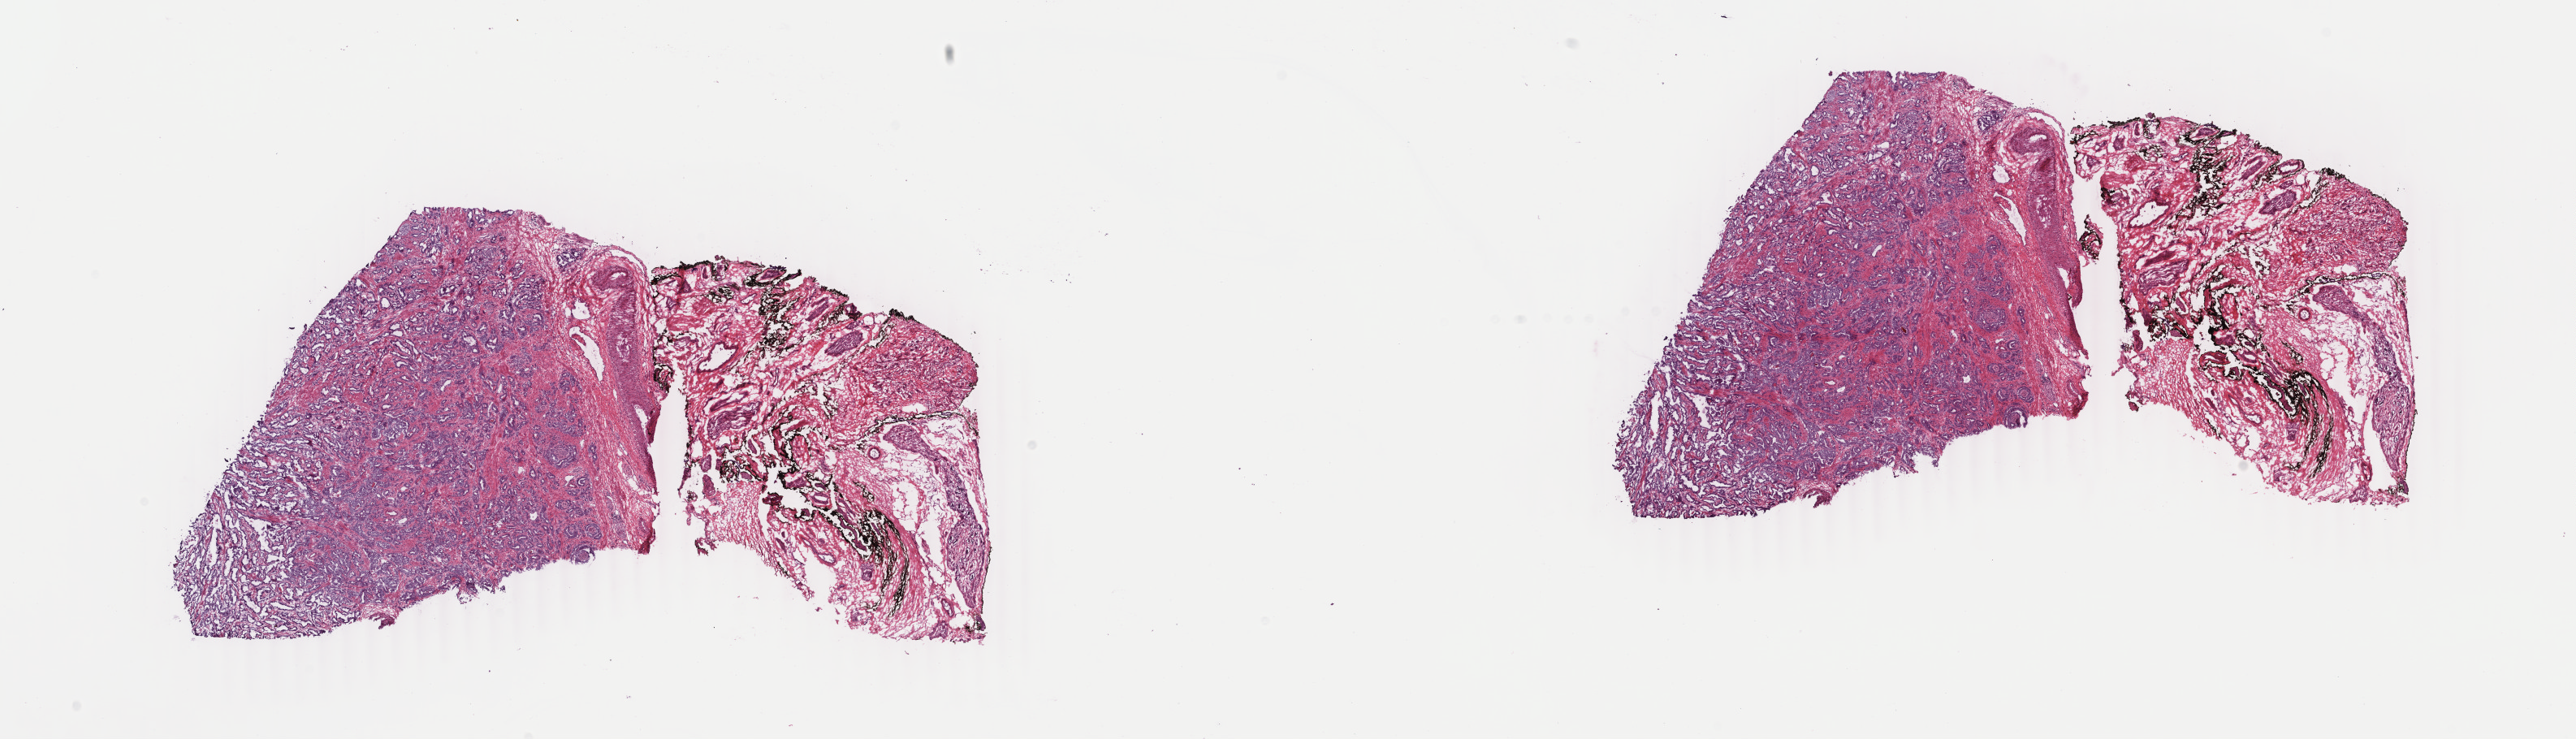
Whole-slide histology image, Hematoxylin and eosin (H&E) stained — shown as a low-resolution overview of the whole scanned area (about 25.2 x 7.2 mm), frozen section from the top of the tissue portion, prostate, primary tumour sample. Patient: male, age at initial diagnosis 56 years. Gleason score: 7 (3+4). Composition of this section per pathologist review: tumour cells 50%, tumour nuclei 60%, normal cells 30%, stromal cells 20%, necrosis 0%. Infiltration values recorded for this section: lymphocyte infiltration 0%, monocyte infiltration 0%, neutrophil infiltration 0%.
* histologic diagnosis: Adenocarcinoma, NOS